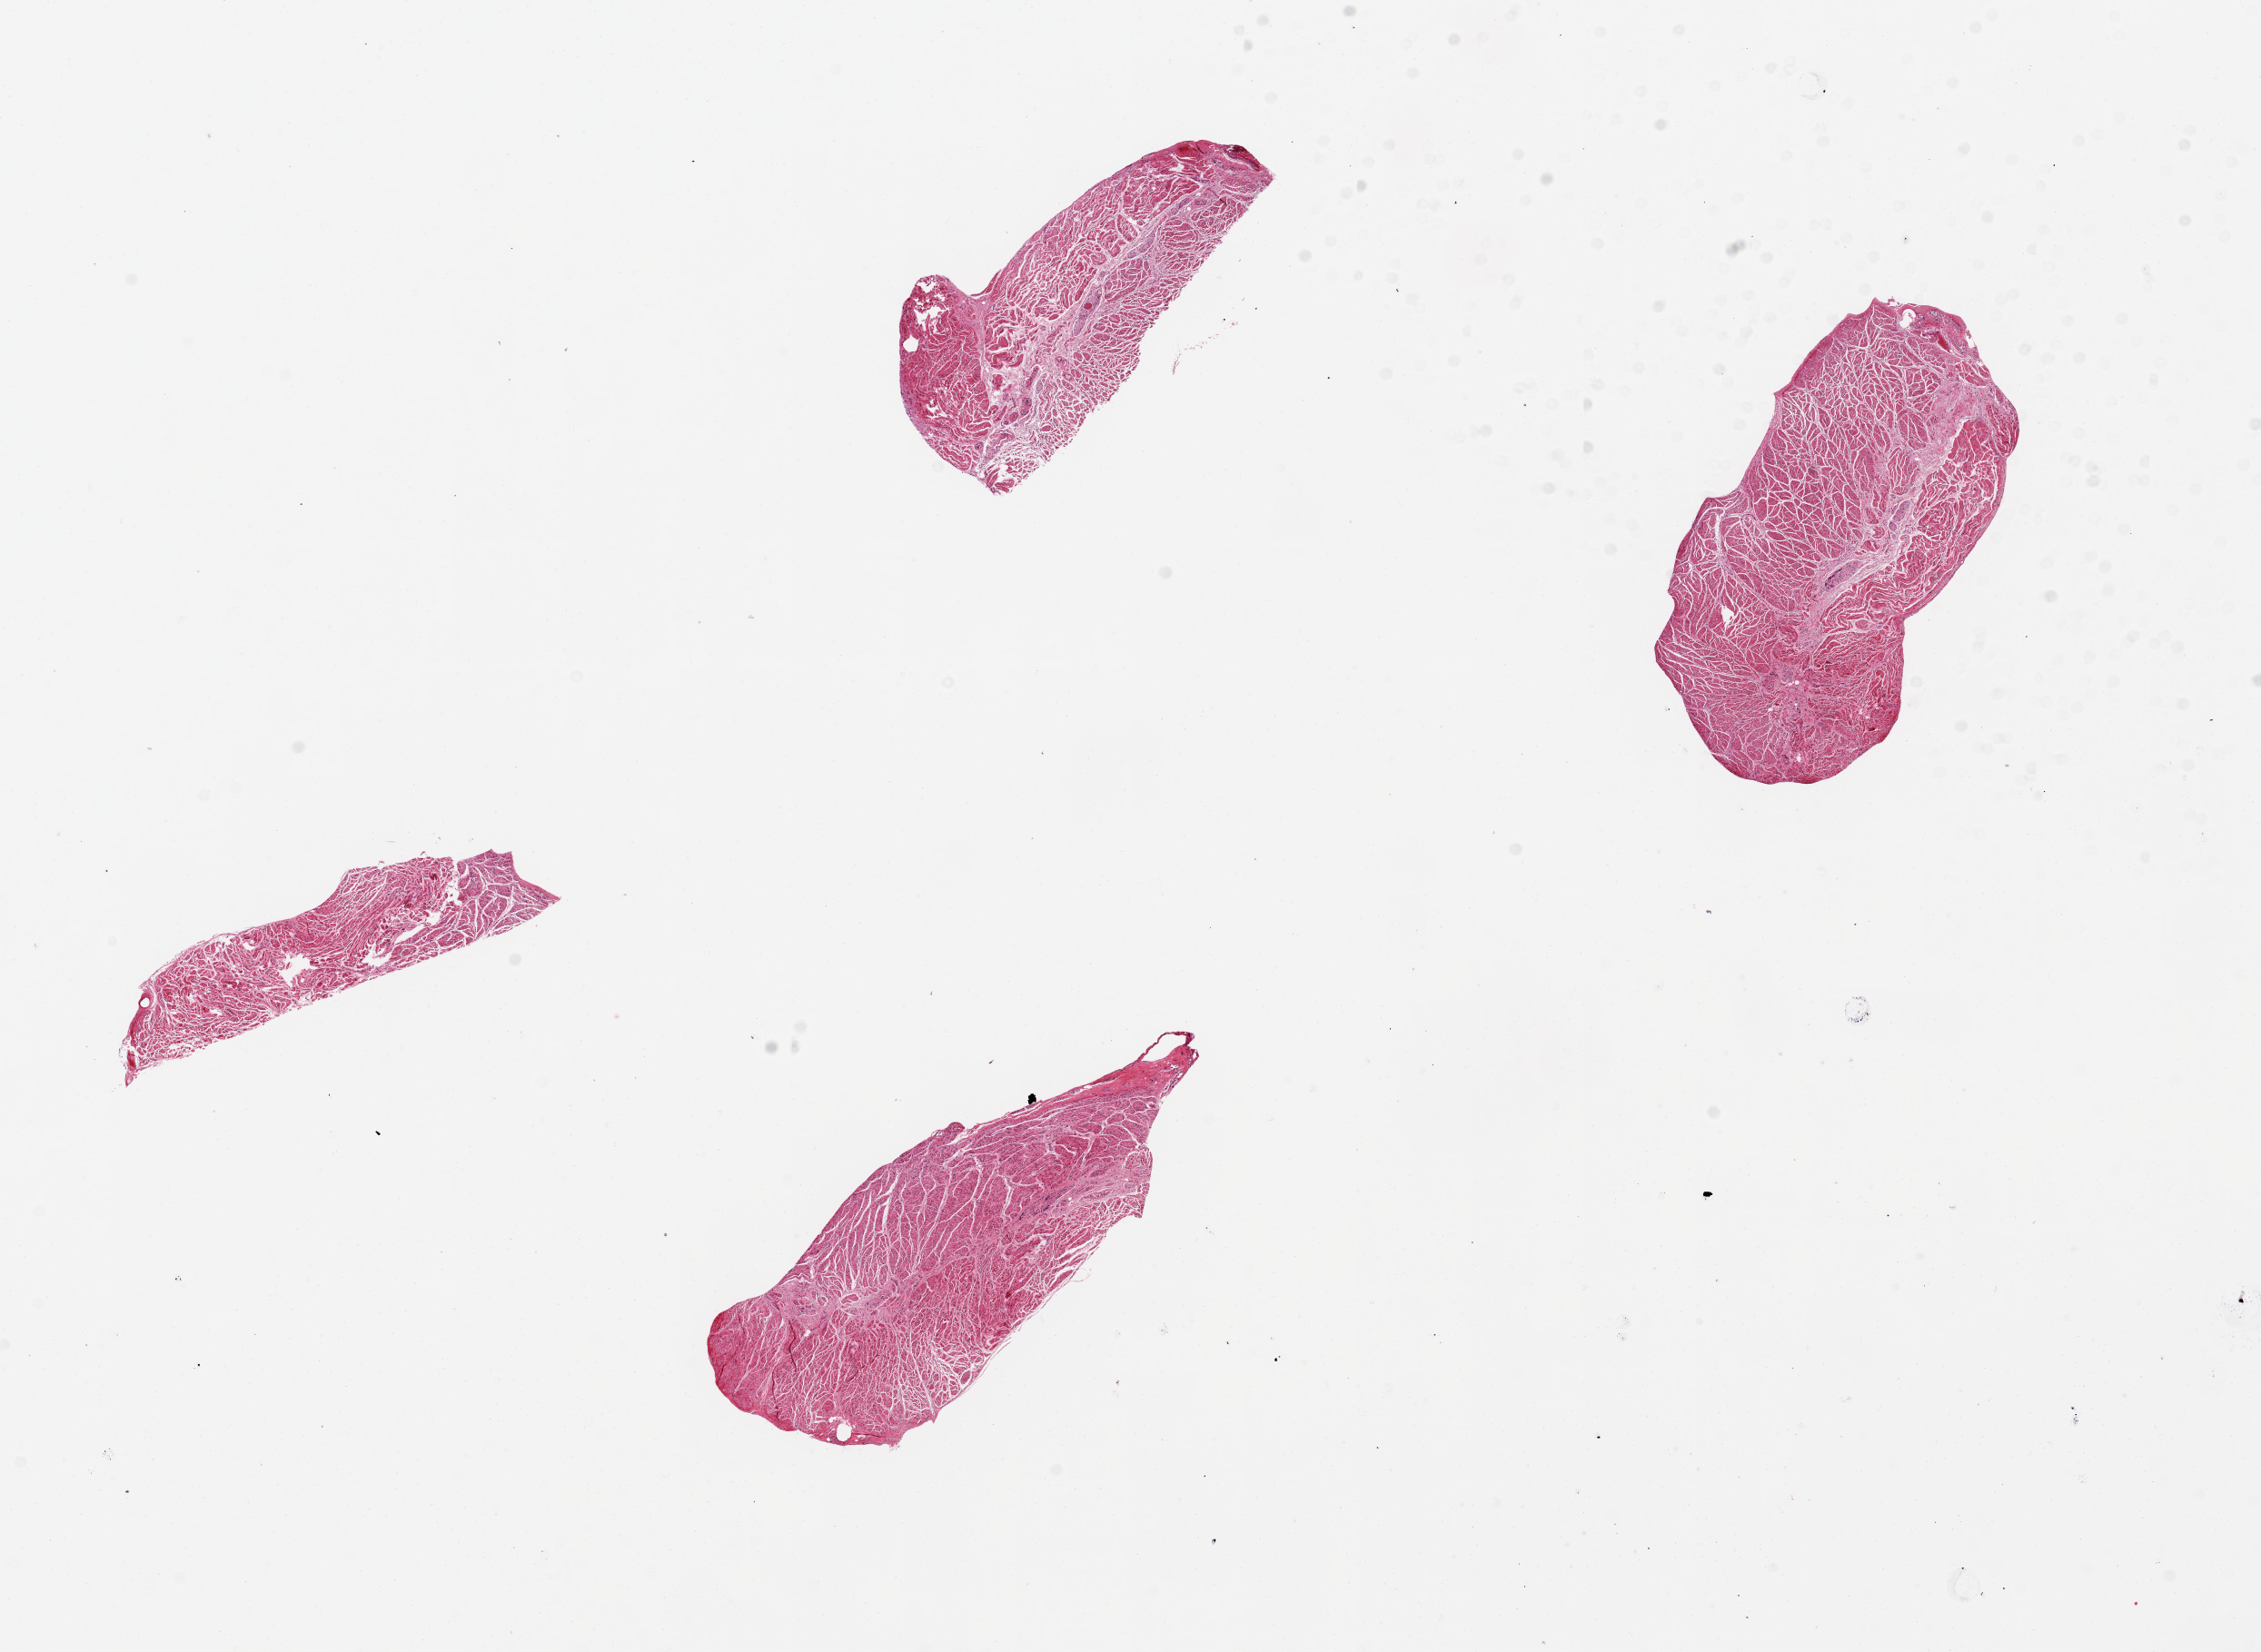
Hematoxylin and eosin (H&E) whole-slide image, a low-resolution overview of the entire scanned area, about 19.7 x 14.4 mm (acquisition: 20x scan); PAXgene-fixed, paraffin-embedded tissue; section of gastroesophageal junction (target tissue); tissue donor sample. Male donor.
* pathologist's review note for this sample: 4 pieces, up to 5x2mm; only muscle, good dissection